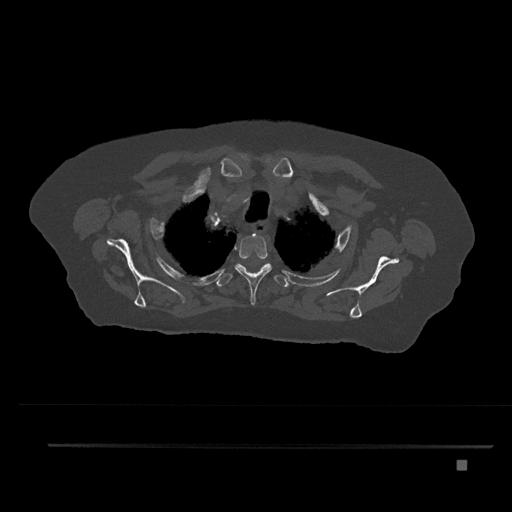
CT including the spine, one axial slice; slice 660 of 797 in the series (ordered by position); reconstruction kernel Br40s/3; 120 kVp; bone window (W 1800 / L 400 HU); 512 × 512 image matrix, field of view 437 × 437 mm. Patient: female, 76 years. From the clinical record (not read from this slice): primary cancer: lung; vertebrae with lytic lesions (as recorded): T11, L3.
Outlined on this slice (semi-automatically segmented with operator editing):
- T1 vertebra: bounding box (x1, y1, x2, y2) in pixels: (253, 233, 255, 235)
- T2 vertebra: (234, 233, 272, 305)
- T3 vertebra: (216, 263, 289, 287)